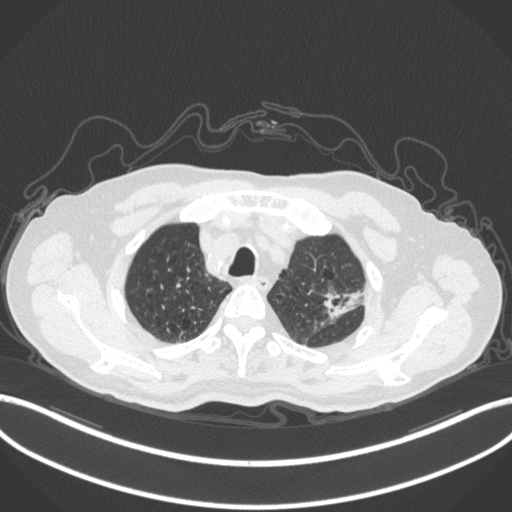
Chest CT, one axial slice. Slice 254 of 331 in the series (ordered by position). Reconstruction kernel B31f. 120 kVp. Lung window (W 1500 / L -600 HU). 1 mm slice thickness. 512 × 512 image matrix, field of view 400 × 400 mm. Male patient, age 79 years. From the clinical record (not read from this slice): clinical TNM (as recorded): T2a N1 M1.
Structures marked on this image (bounding box drawn by a radiologist):
- lung tumour (recorded histology: adenocarcinoma): box from (x=317, y=285) to (x=371, y=319) px